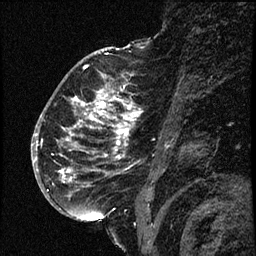
Breast MRI (dynamic contrast-enhanced), one sagittal slice. Position 40 of 66 along the scan axis. Dynamic contrast-enhanced study with each time point stored as its own series, time point 2 of 3 at this slice position (early post-contrast, ordered by acquisition time). 1.5 T. TE 4.2 ms, TR 17.6 ms. 2 mm slice thickness. 256 × 256 image matrix, field of view 200 × 200 mm. Female patient. Case-level facts recorded for this patient, not image findings: setting: breast cancer imaged before/during neoadjuvant chemotherapy; receptor status: HER2-positive.
Structures marked on this image (semi-automatically segmented with operator editing):
- analysis volume of interest (the breast-tissue region the enhancement analysis was run in; not a lesion): box from (x=52, y=69) to (x=147, y=209) px
- tumour enhancement mask (voxels above the 100 % enhancement threshold inside the analysis volume of interest): (x=61, y=88)–(x=139, y=186)